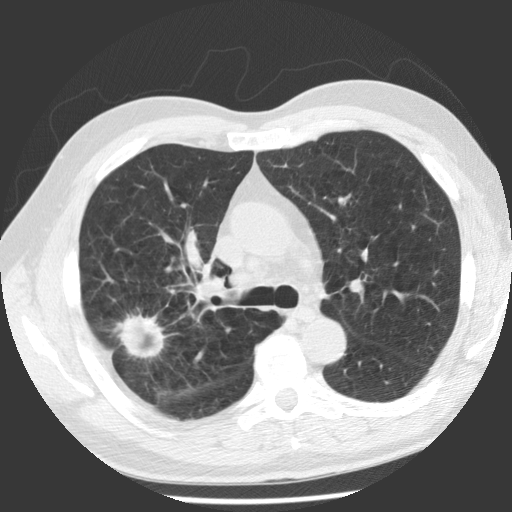
Low-dose screening chest CT, one axial slice. Slice 73 of 112 in the series (ordered by position). 140 kVp. Lung window (W 1500 / L -600 HU). 2.5 mm slice thickness. 512 × 512 image matrix, field of view 344 × 344 mm.
Outlined on this slice (outlined manually by an expert reader):
- lesion 1 (tumor, upper lobe of right lung): bounding box [x1, y1, x2, y2] px = [116, 314, 165, 359]